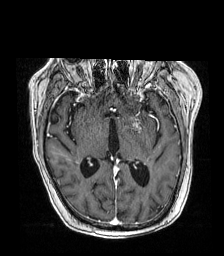
Brain MRI from a brain-tumour surgery series, one axial slice. Slice 94 of 192 in the series (ordered by position). T1-weighted post-contrast. 1 mm slice thickness. 224 × 256 image matrix, field of view 219 × 250 mm. Case-level facts recorded for this patient, not image findings: histopathology: Metastatic carcinoma from lung primary.
Structures marked on this image (manually delineated by an expert):
- tumour: box from (x=117, y=118) to (x=148, y=126) px